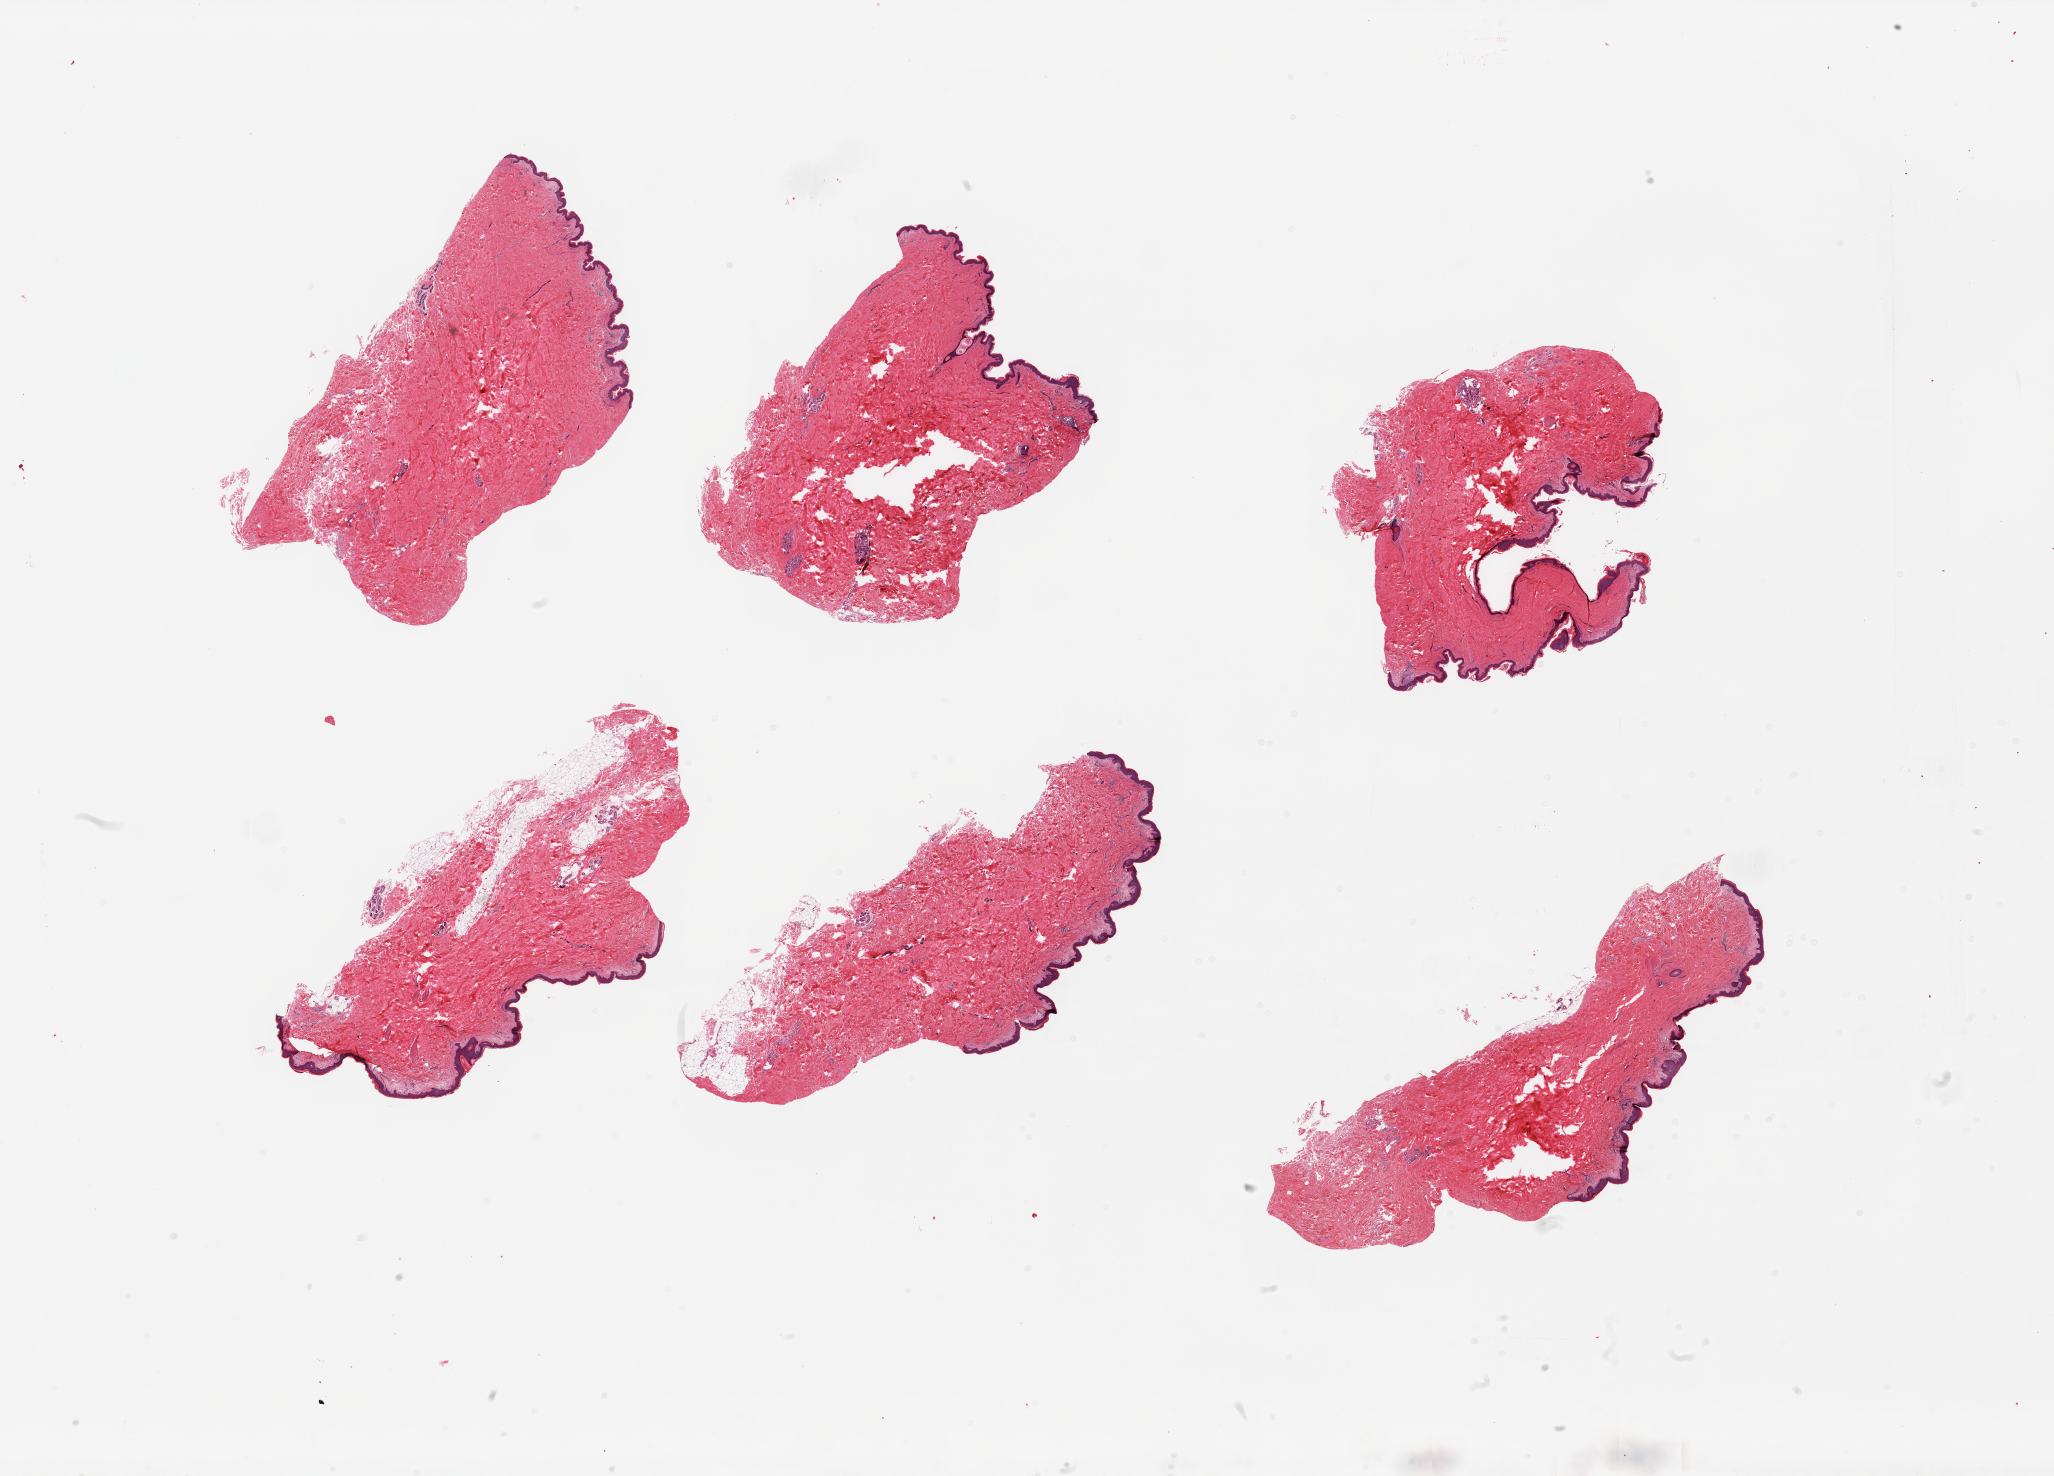
Whole-slide image, H&E stain, low-resolution overview of the scanned area, about 32.5 x 23.3 mm. PAXgene-fixed paraffin-embedded (PFPE) section. Sampled site (target tissue): skin of suprapubic region. Donor tissue sample. Donor sex: male.
Pathologist's review note for this sample: 6 pieces, trace adherent fat, squamous epithelium is ~70 microns.